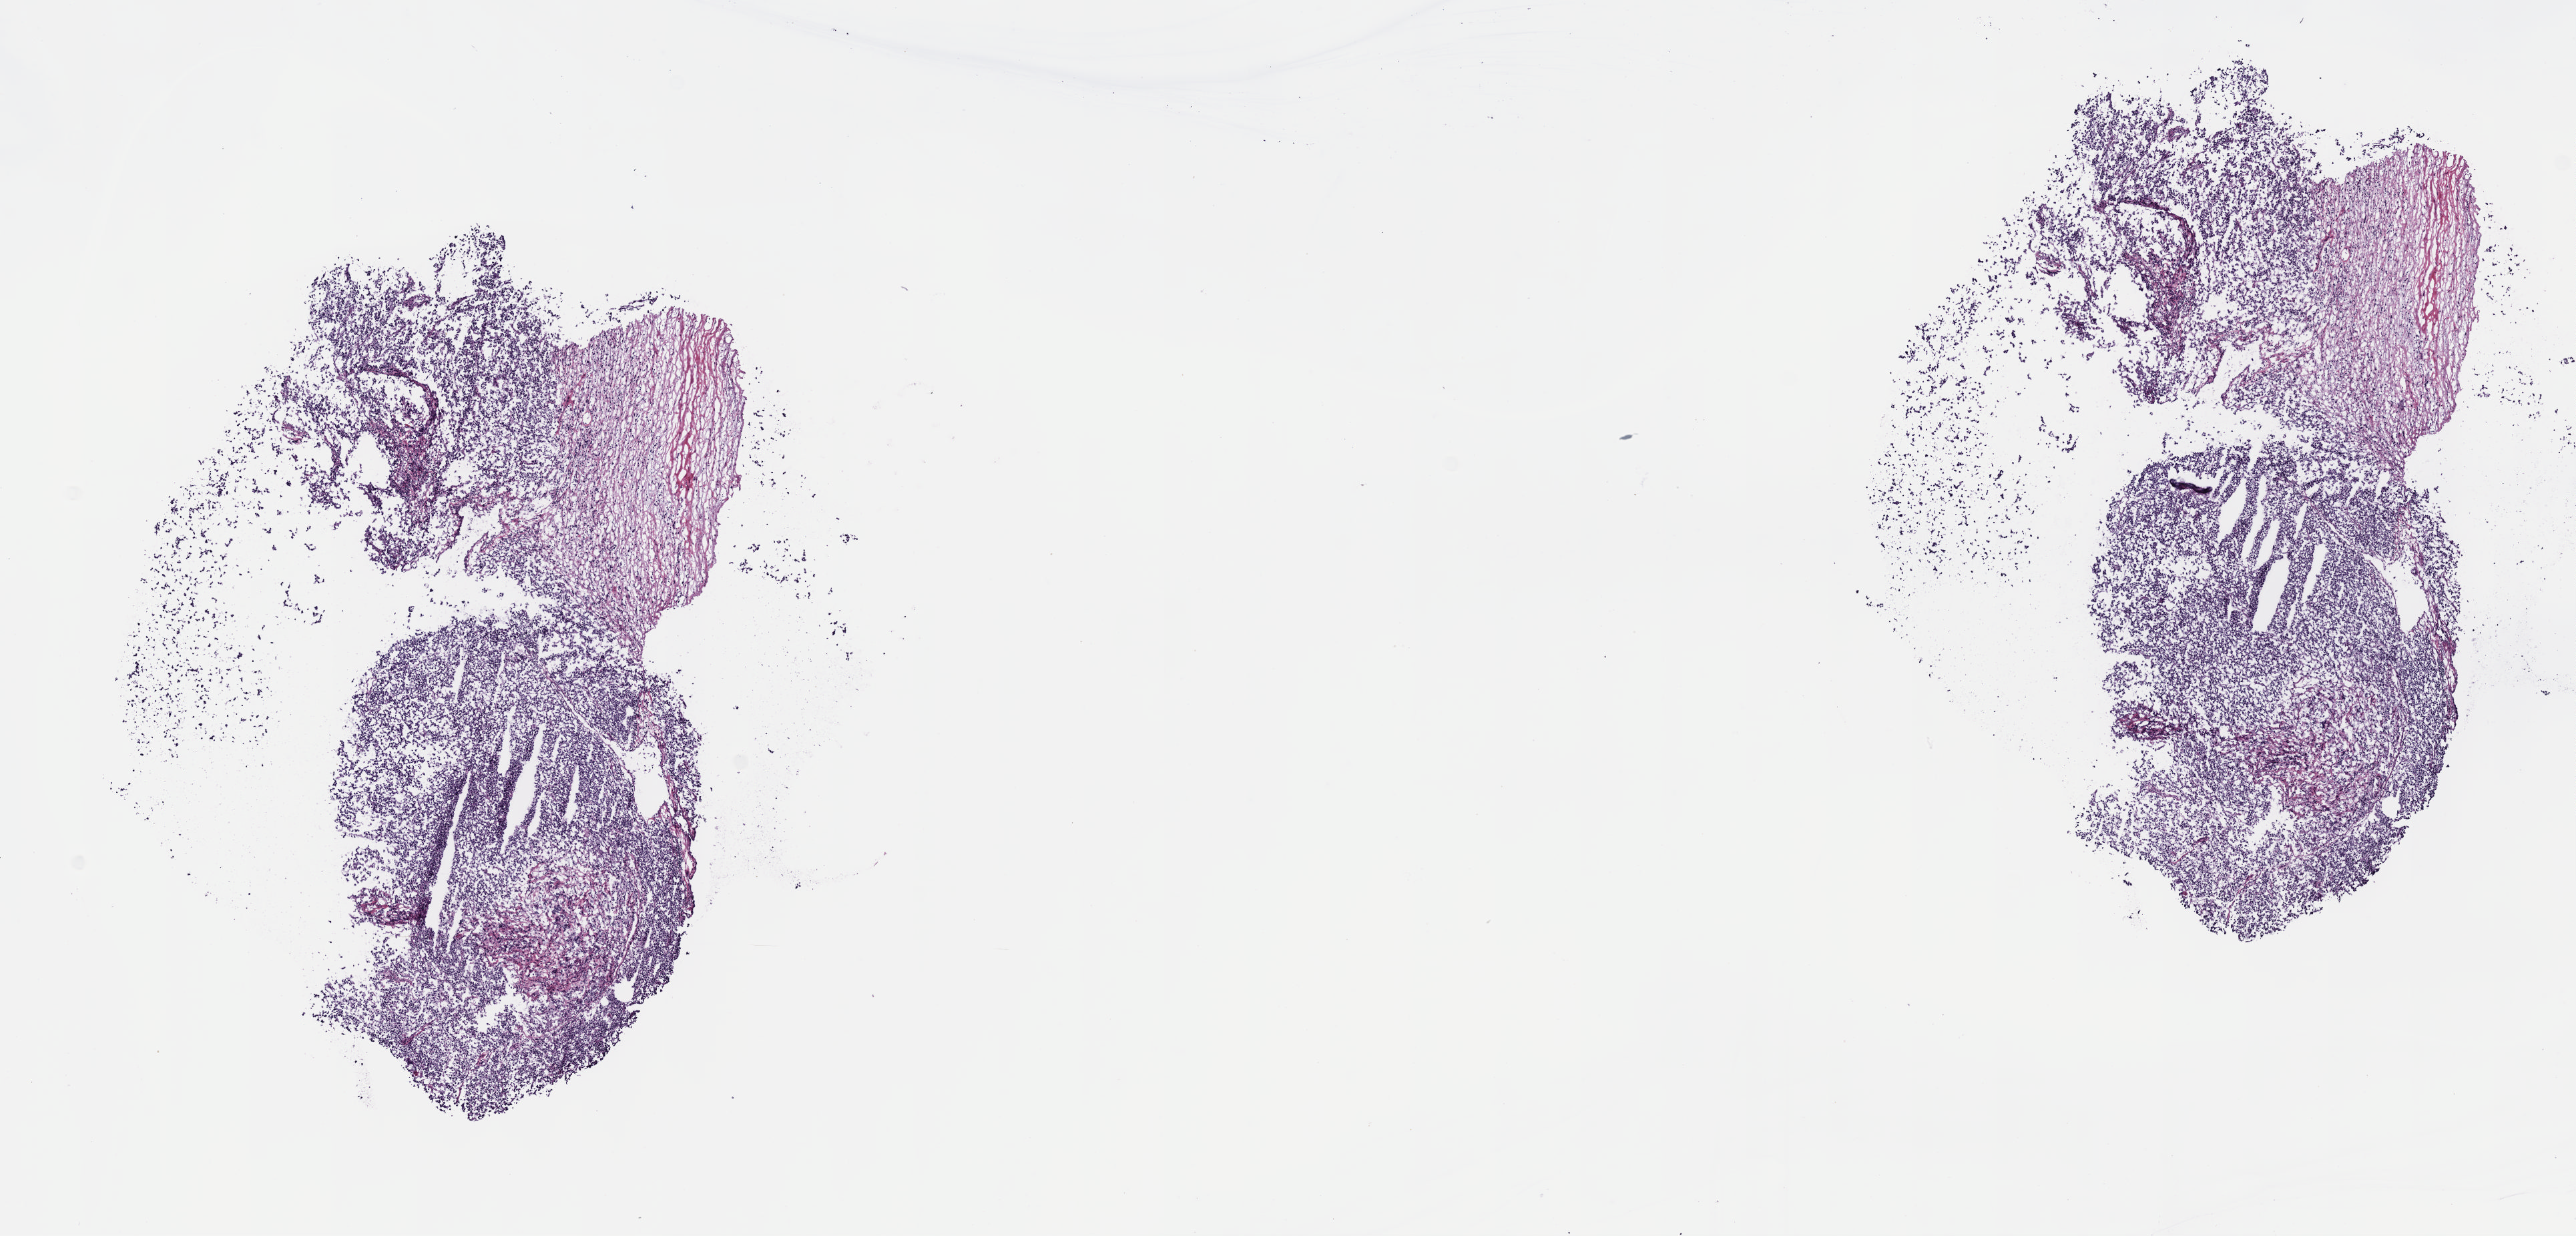
Digitized H&E tissue section (whole slide) — whole scanned area (about 15.6 x 7.5 mm, acquisition: 40x scan) shown as a low-resolution overview, frozen section from the top of the tissue portion, primary tumour sample from the testis. Patient: male, age at initial diagnosis 45 years. Composition of this section per pathologist review: tumour cells 100%, tumour nuclei 75%, normal cells 0%, stromal cells 0%, necrosis 0%. Inflammatory infiltration, as recorded: lymphocyte infiltration 1%, monocyte infiltration 0%, neutrophil infiltration 0%.
AJCC pathologic stage: IB. Pathologic diagnosis: Seminoma, NOS.